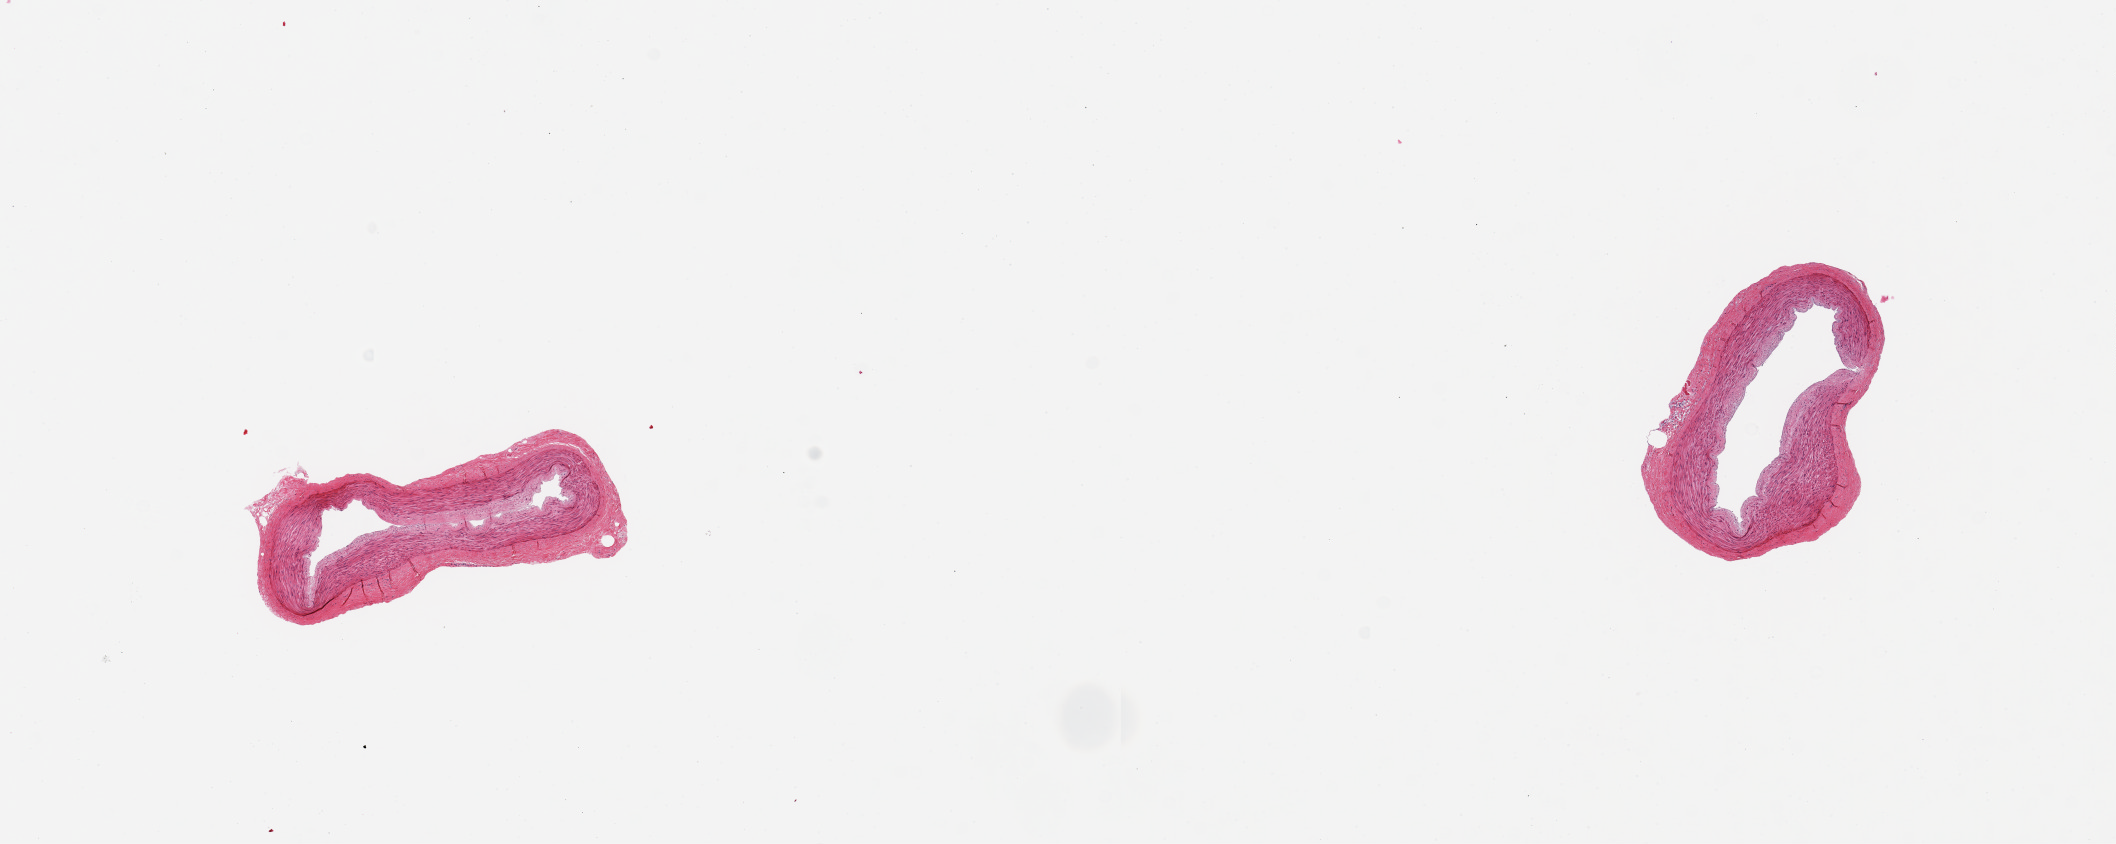
Hematoxylin and eosin (H&E) whole-slide image — low-resolution overview of the scanned area, about 16.7 x 6.7 mm; PAXgene-fixed paraffin-embedded (PFPE) section; target tissue: tibial artery; donor tissue sample. Male donor.
- pathologist's review note for this sample: 2 pieces, 3x1 & 2.5x2mm; good clean specimen